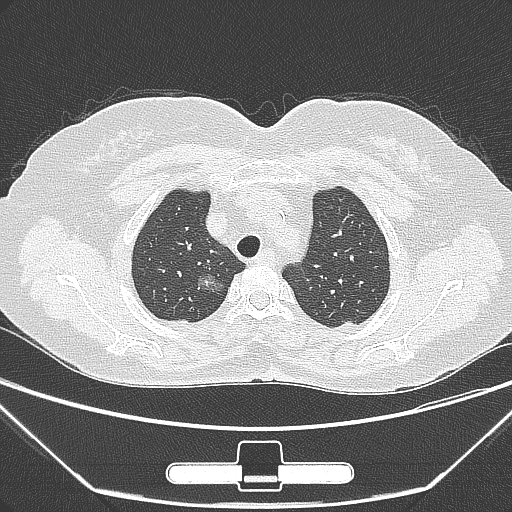
Chest CT, one axial slice; slice 229 of 275 in the series (ordered by position); 120 kVp; lung window (W 1500 / L -600 HU); 1 mm slice thickness; 512 × 512 image matrix. Female patient, age 63 years. Case-level facts recorded for this patient, not image findings: clinical TNM (as recorded): T1a N0 M0.
Structures marked on this image (bounding box drawn by a radiologist):
- lung tumour (recorded histology: adenocarcinoma): bounding box <197,271,227,296> (left, top, right, bottom; pixels)